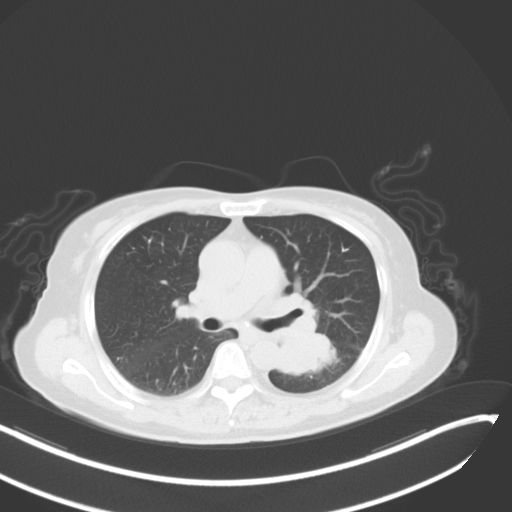
Chest CT, one axial slice; position 23 of 48 along the scan axis; lung window (W 1500 / L -600 HU); 5 mm slice thickness; 512 × 512 image matrix, field of view 400 × 400 mm. Patient: female, 64 years. From the clinical record (not read from this slice): clinical TNM (as recorded): T3 N1 M1; histopathological grade: G3.
Outlined on this slice (rectangle marked by the reading radiologist):
- lung tumour (recorded histology: small cell carcinoma): bounding box <266,319,335,377> (left, top, right, bottom; pixels)